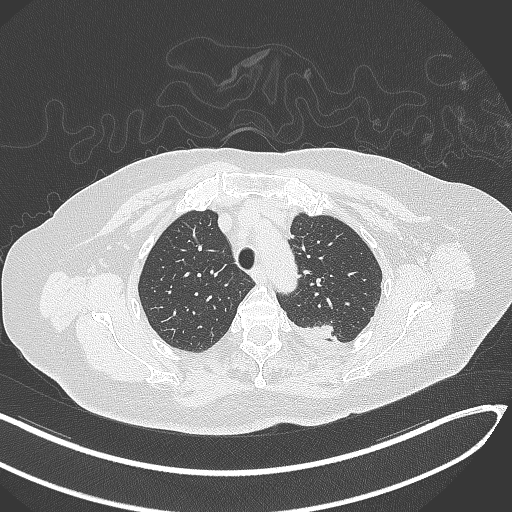
Chest CT, one axial slice; position 254 of 270 along the scan axis; reconstruction kernel B70f; 120 kVp; lung window (W 1500 / L -600 HU); 1 mm slice thickness; 512 × 512 image matrix. Patient: female, 76 years. From the clinical record (not read from this slice): clinical TNM (as recorded): T1c N0 M0.
Annotated regions visible in this slice (rectangle marked by the reading radiologist):
- lung tumour (recorded histology: adenocarcinoma): bounding box [x1, y1, x2, y2] px = [312, 315, 337, 342]